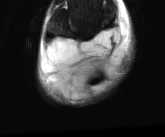
MRI of an extremity soft-tissue mass, one axial slice. Position 13 of 81 along the scan axis. T2-weighted fat-saturated. MR volume resampled by the dataset authors to the PET/CT grid (not the native acquisition matrix). 165 × 137 image matrix, field of view 161 × 134 mm. Male patient. From the clinical record (not read from this slice): histological type: liposarcoma - round cell; grade: high; site of the primary tumour: right calf.
Outlined on this slice (expert contour drawn on MRI and transferred to this co-registered scan by the dataset authors):
- gross tumour volume (mass): box from (x=41, y=29) to (x=127, y=101) px